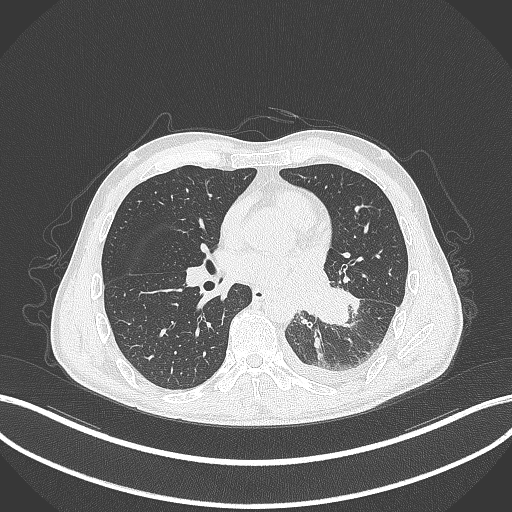
Chest CT, one axial slice; position 148 of 295 along the scan axis; reconstruction kernel B70f; 120 kVp; lung window (W 1500 / L -600 HU); 1 mm slice thickness; 512 × 512 image matrix. Patient: male, 47 years. Case-level facts recorded for this patient, not image findings: clinical TNM (as recorded): T3 N1 M1c; histopathological grade: G3.
Structures marked on this image (rectangle marked by the reading radiologist):
- lung tumour (recorded histology: small cell carcinoma): bounding box (x1, y1, x2, y2) in pixels: (312, 285, 350, 325)